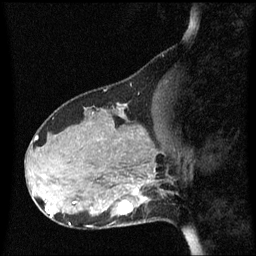
Breast MRI (dynamic contrast-enhanced), one sagittal slice; position 21 of 60 along the scan axis; dynamic contrast-enhanced series, image 2 of 3 at this slice position (ordered by acquisition); 1.5 T; TE 4.2 ms, TR 8.4 ms; 256 × 256 image matrix, field of view 210 × 210 mm. Female patient, age 31 years. Case-level facts recorded for this patient, not image findings: setting: breast cancer imaged before/during neoadjuvant chemotherapy; receptor status: HR-positive, HER2-negative.
Structures marked on this image (semi-automatically segmented with operator editing):
- analysis volume of interest (the breast-tissue region the enhancement analysis was run in; not a lesion): bounding box (x1, y1, x2, y2) in pixels: (98, 175, 165, 228)
- tumour enhancement mask (voxels above the 70 % enhancement threshold inside the analysis volume of interest): (119, 190, 146, 216)